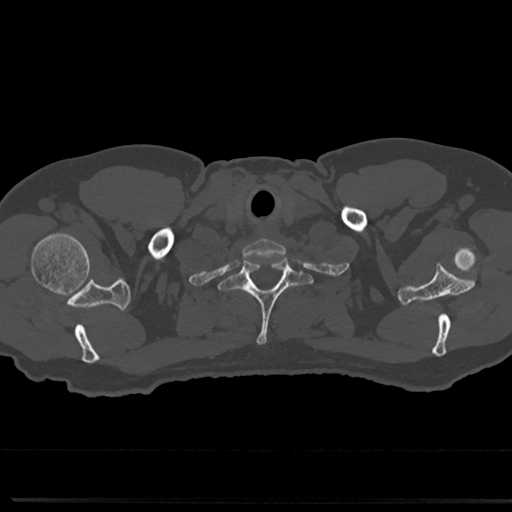
CT including the spine, one axial slice; position 679 of 817 along the scan axis; bone window (W 1800 / L 400 HU); 0.5 mm slice thickness; 512 × 512 image matrix. Patient: male, 61 years. Case-level facts recorded for this patient, not image findings: primary cancer: prostate.
Annotated regions visible in this slice (semi-automatic segmentation, software-assisted and operator-edited):
- T1 vertebra: bounding box [x1, y1, x2, y2] px = [227, 252, 307, 346]
- T2 vertebra: [213, 294, 314, 311]